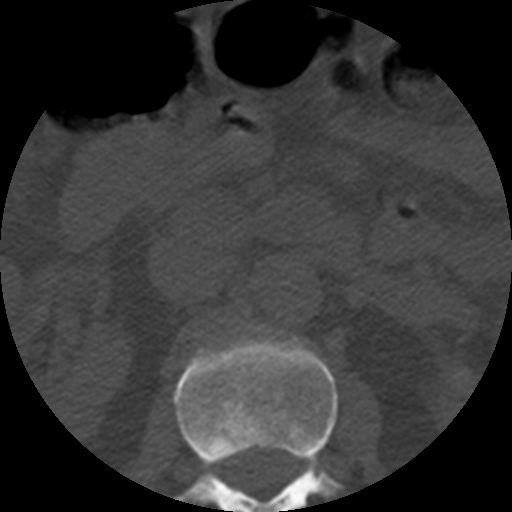
CT including the spine, one axial slice. Slice 177 of 508 in the series (ordered by position). Reconstruction kernel STANDARD. 120 kVp. Bone window (W 1800 / L 400 HU). 1.25 mm slice thickness. 512 × 512 image matrix, field of view 160 × 160 mm. Patient age 57 years. From the clinical record (not read from this slice): primary cancer: prostate.
Annotated regions visible in this slice (semi-automatic segmentation, software-assisted and operator-edited):
- L1 vertebra: bounding box <172,332,343,512> (left, top, right, bottom; pixels)